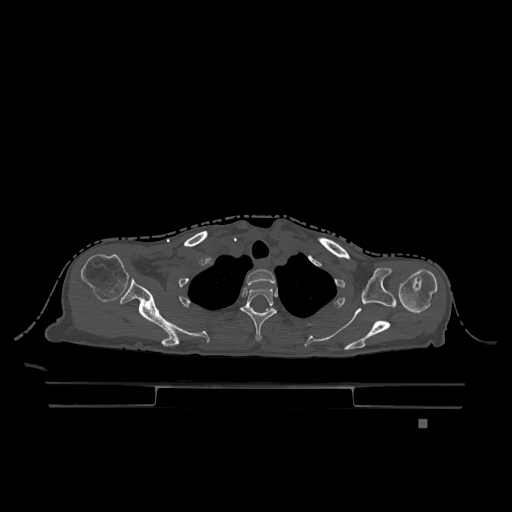
CT including the spine, one axial slice. Position 963 of 1317 along the scan axis. Bone window (W 1800 / L 400 HU). 0.5 mm slice thickness. 512 × 512 image matrix. Patient: female, 74 years. Case-level facts recorded for this patient, not image findings: primary cancer: lung; vertebrae with lytic lesions (as recorded): T1, T4, T5, T6, L4, L5.
Structures marked on this image (semi-automatic segmentation, software-assisted and operator-edited):
- T1 vertebra: bounding box <247,269,276,286> (left, top, right, bottom; pixels)
- T2 vertebra: <241,287,277,341>